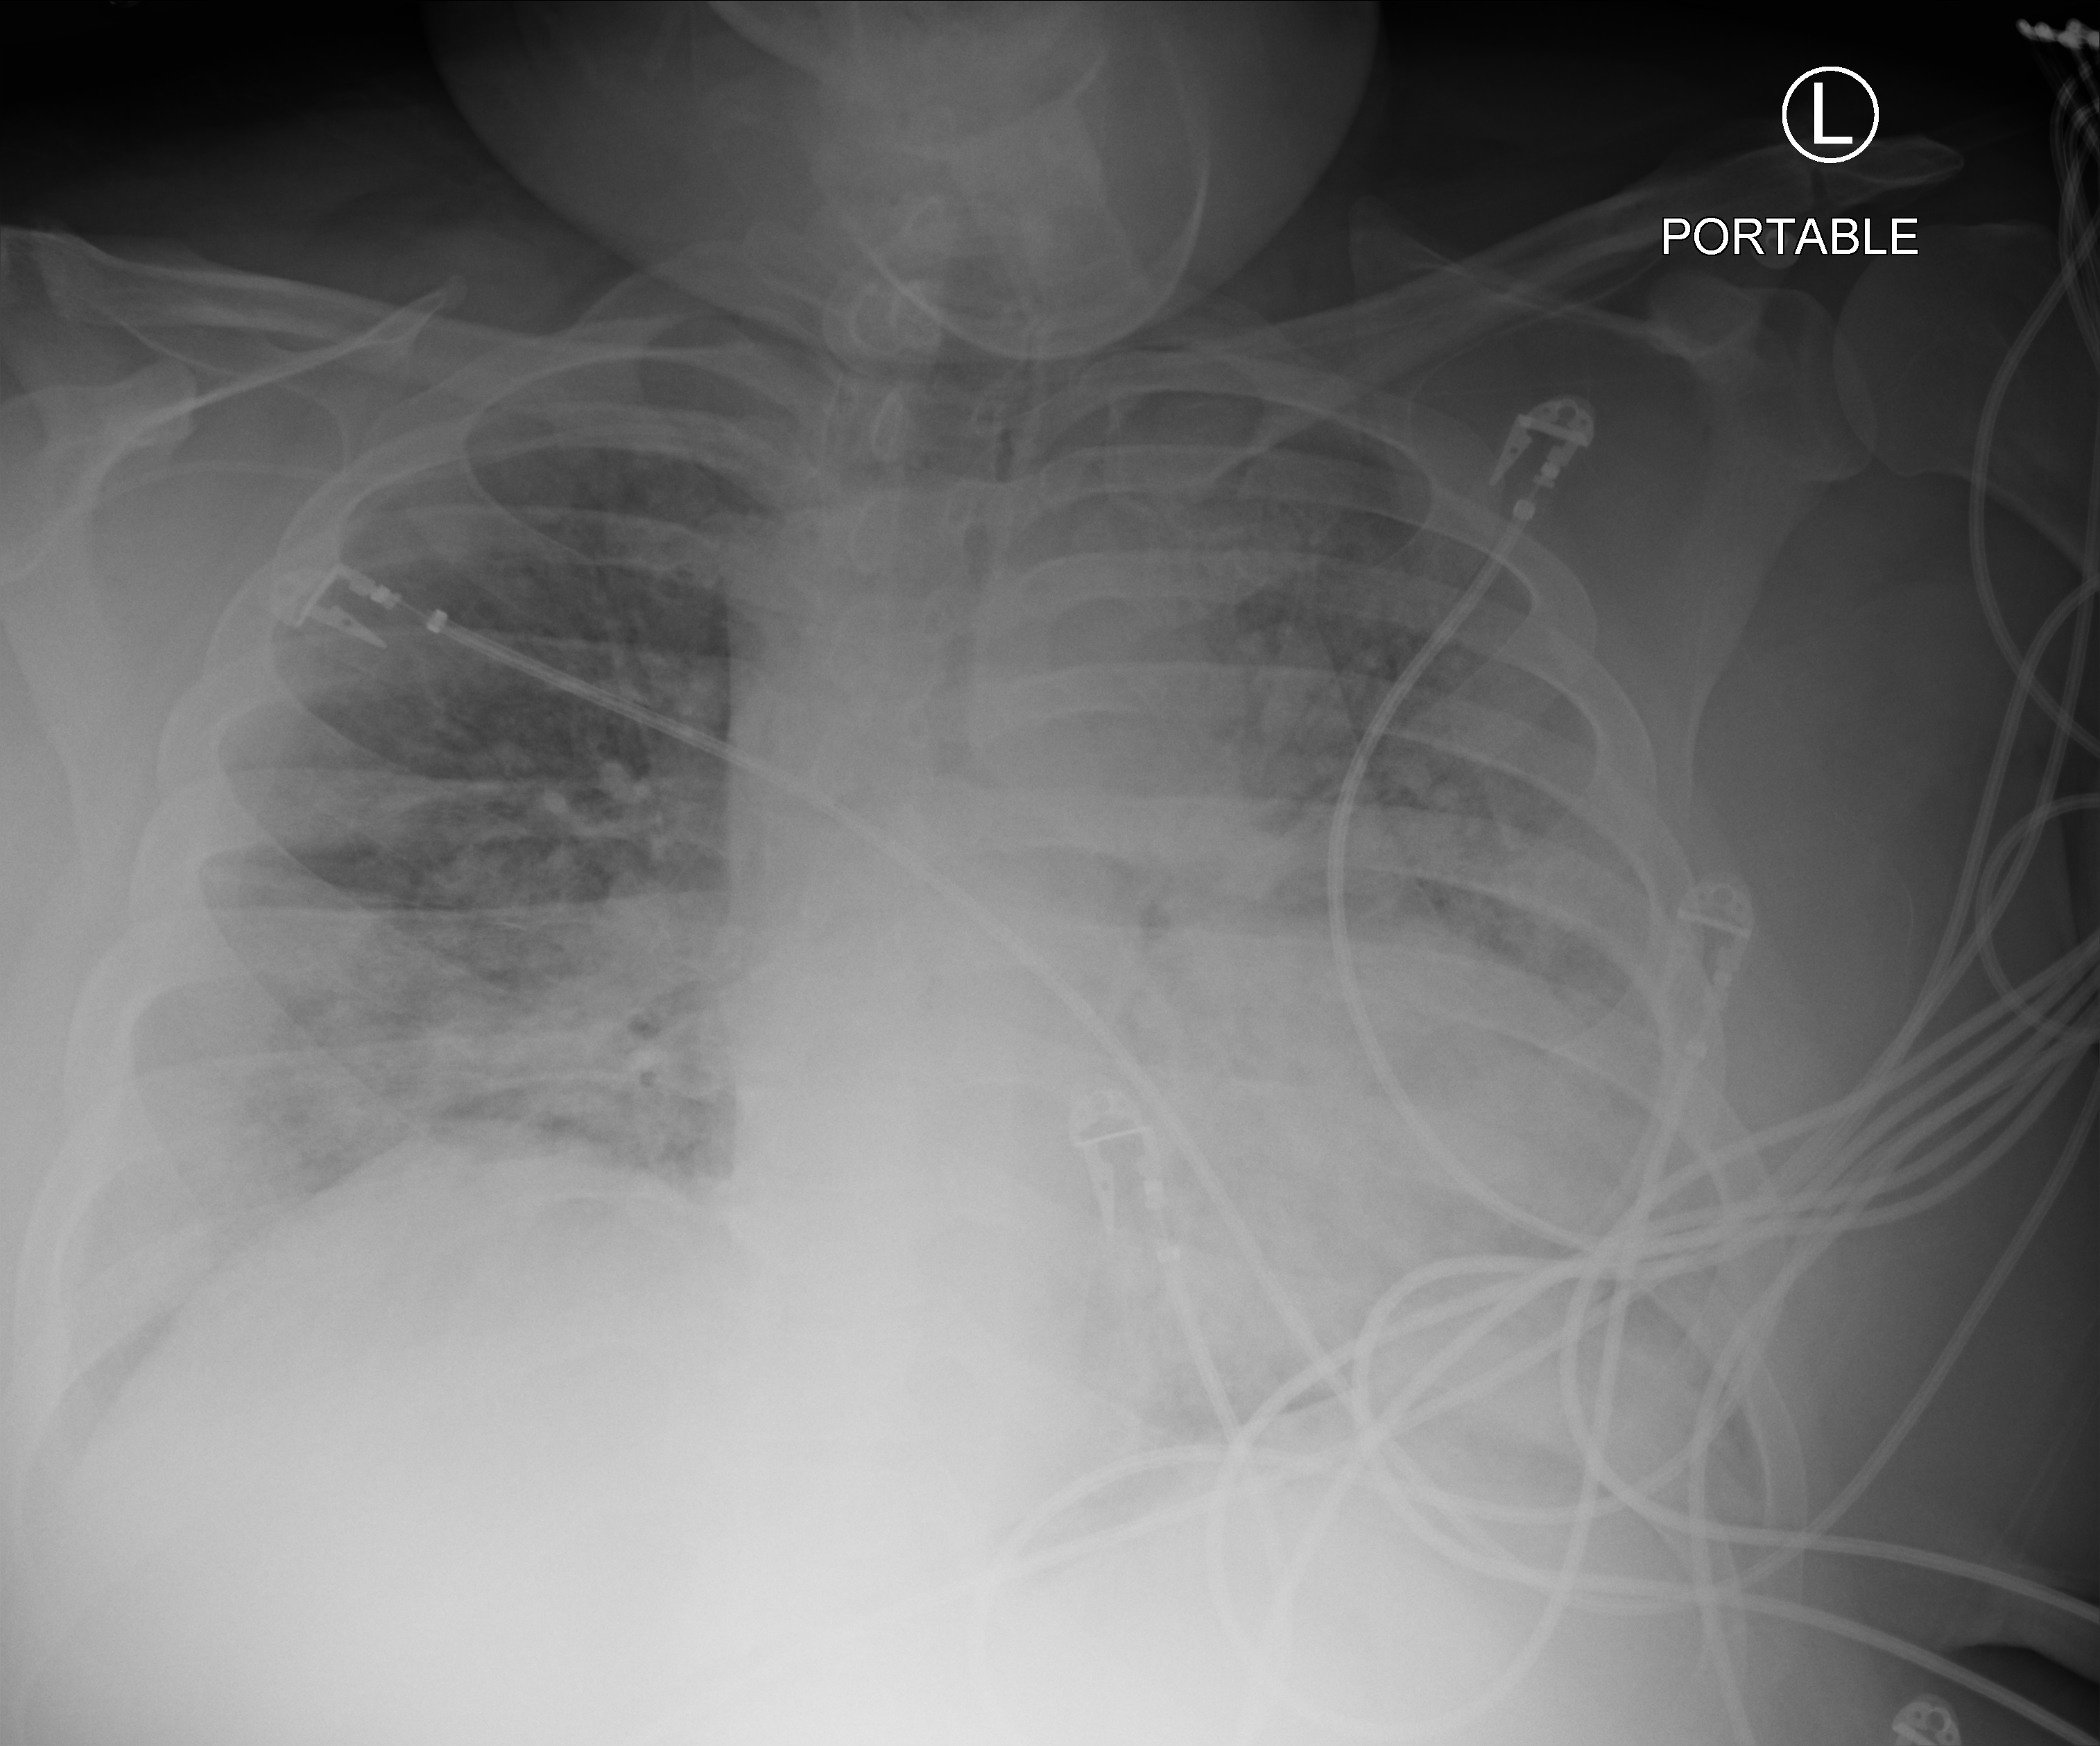
Chest X-ray (portable), anteroposterior (AP) projection. Patient hospitalised with COVID-19, aged 18–59 years.
From the hospital-stay record, not from the radiograph (when in the stay this image was taken is not recorded):
- diabetes (admission record): yes
- admitted to intensive care during this hospital stay: yes
- mechanically ventilated during this hospital stay: yes